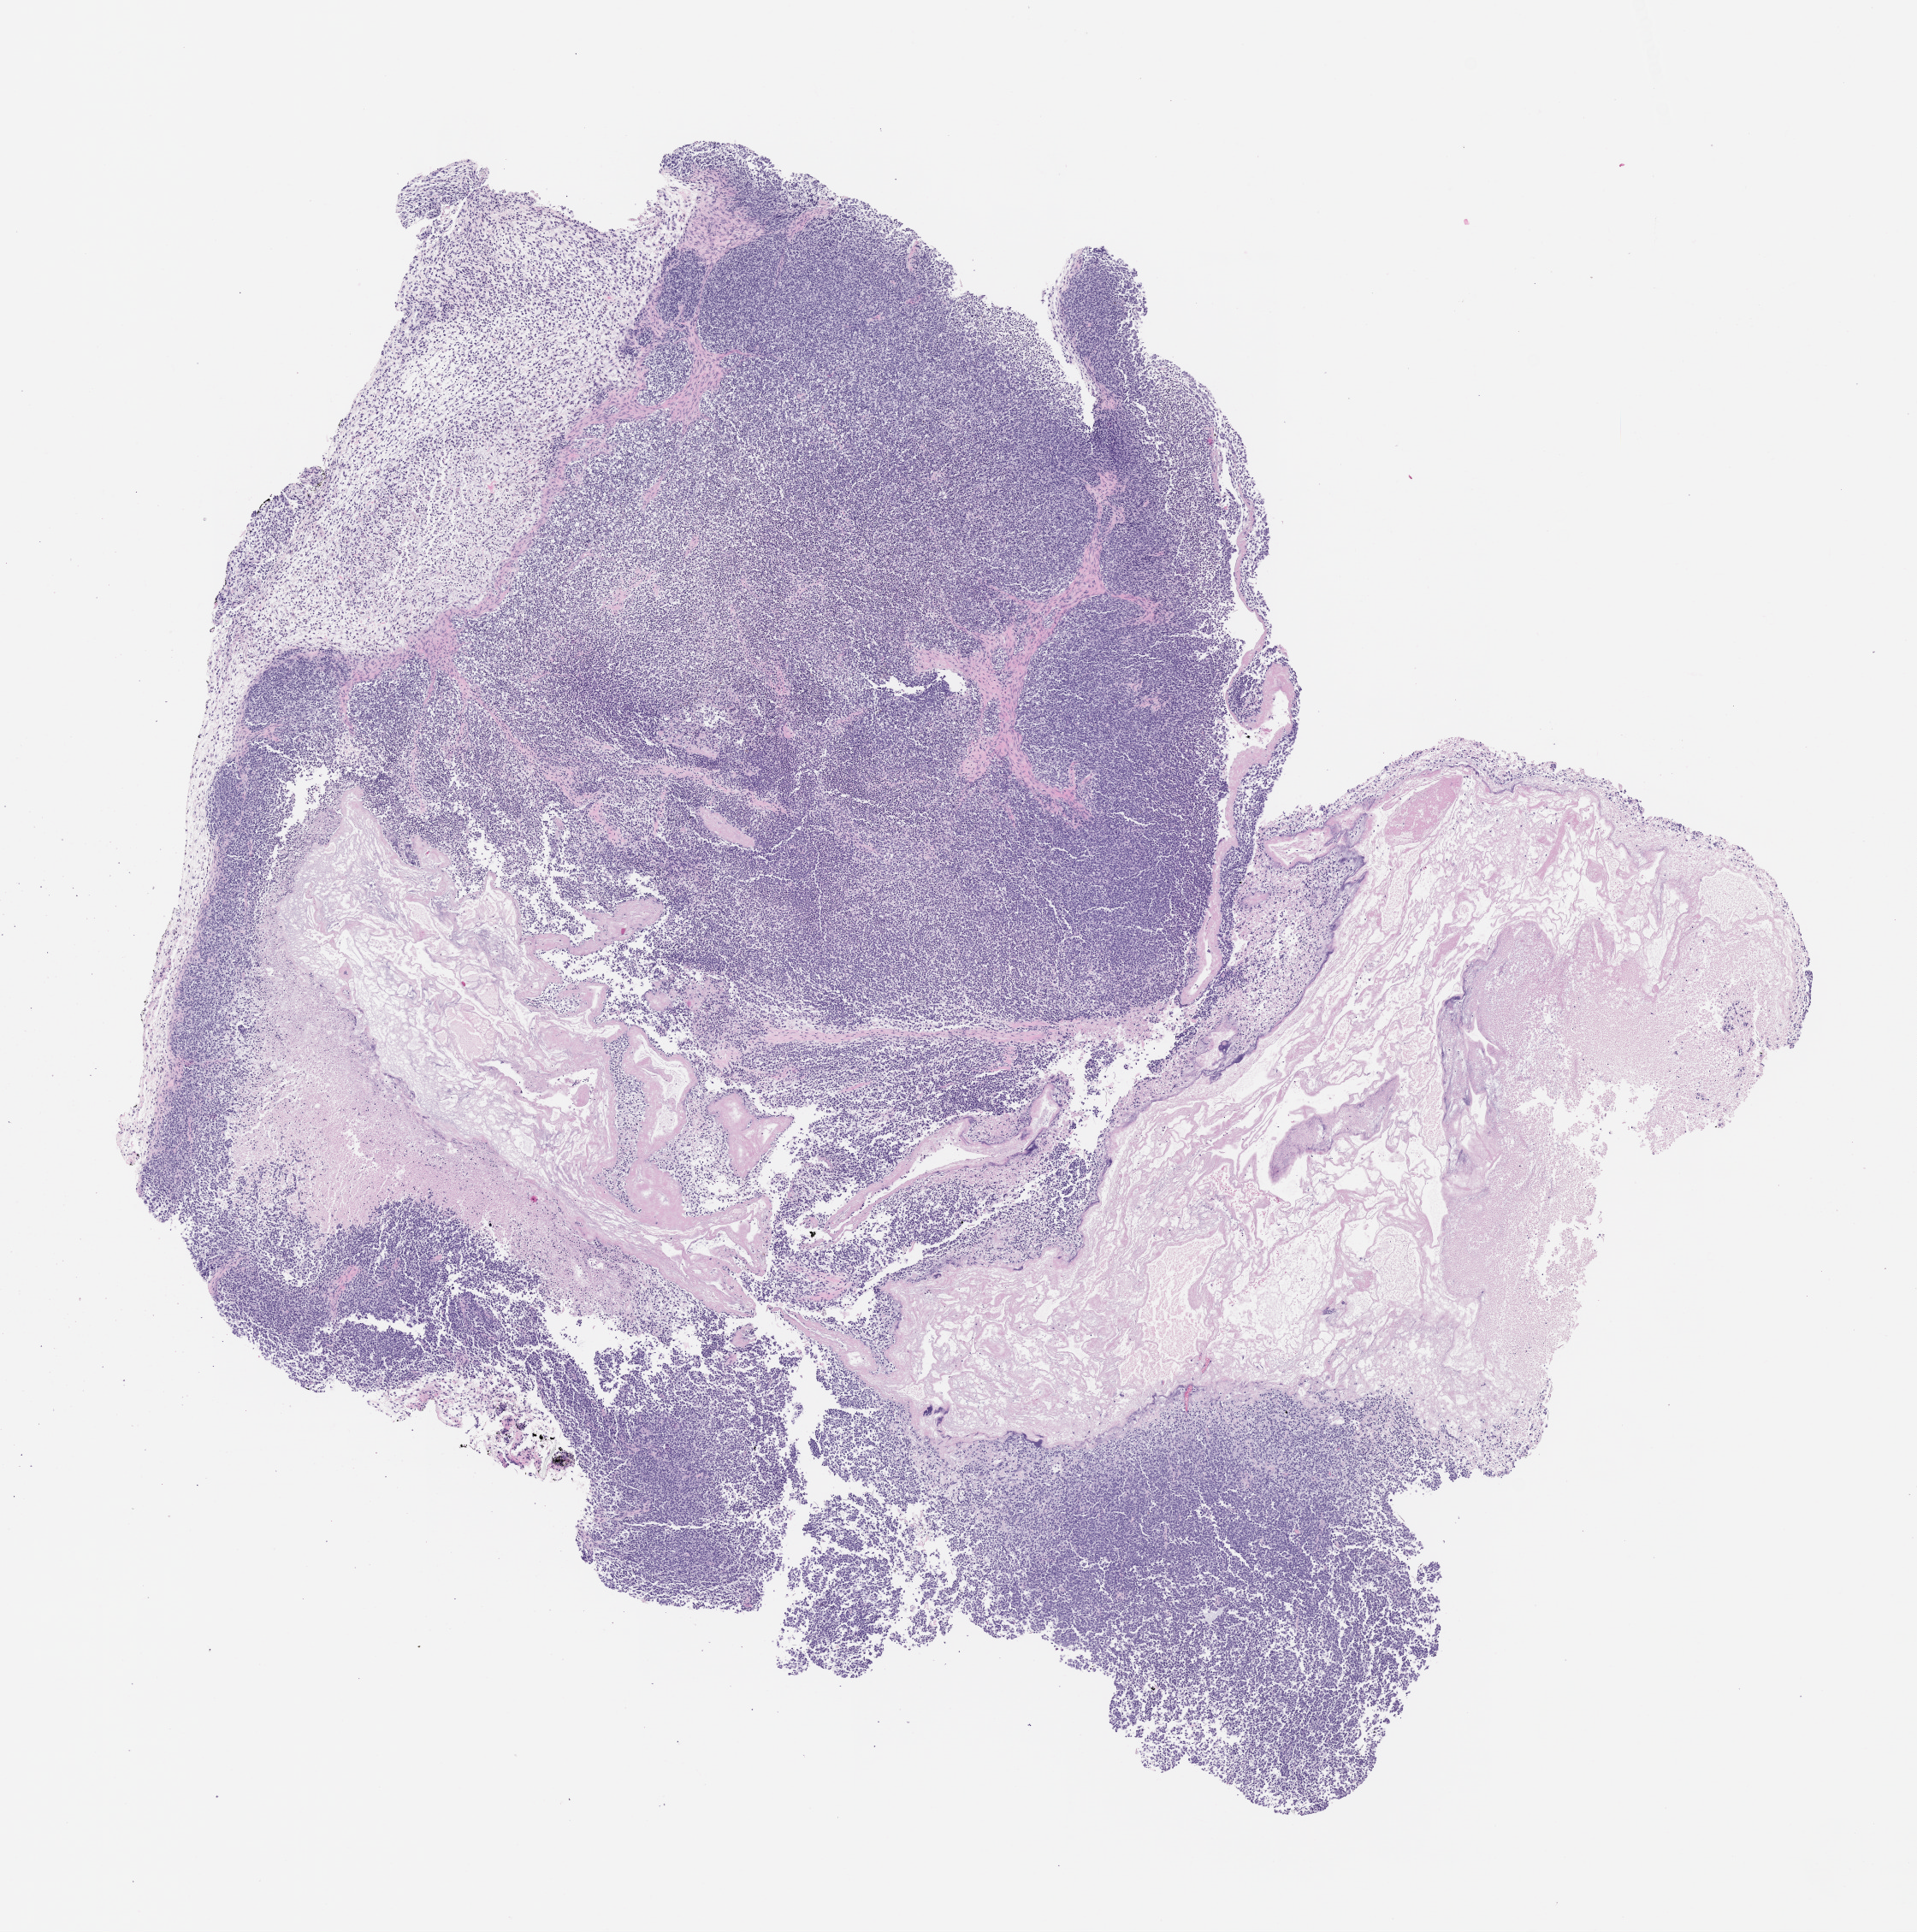
Hematoxylin and eosin (H&E) whole-slide image of a patient-derived xenograft (PDX) tumor grown in a mouse, passage 0, a low-resolution overview of the entire scanned area, about 9.0 x 9.1 mm; formalin-fixed paraffin-embedded section; tumor site category: musculoskeletal.
• originating patient diagnosis: Ewing Sarcoma|Primitive Neuroectodermal Tumor